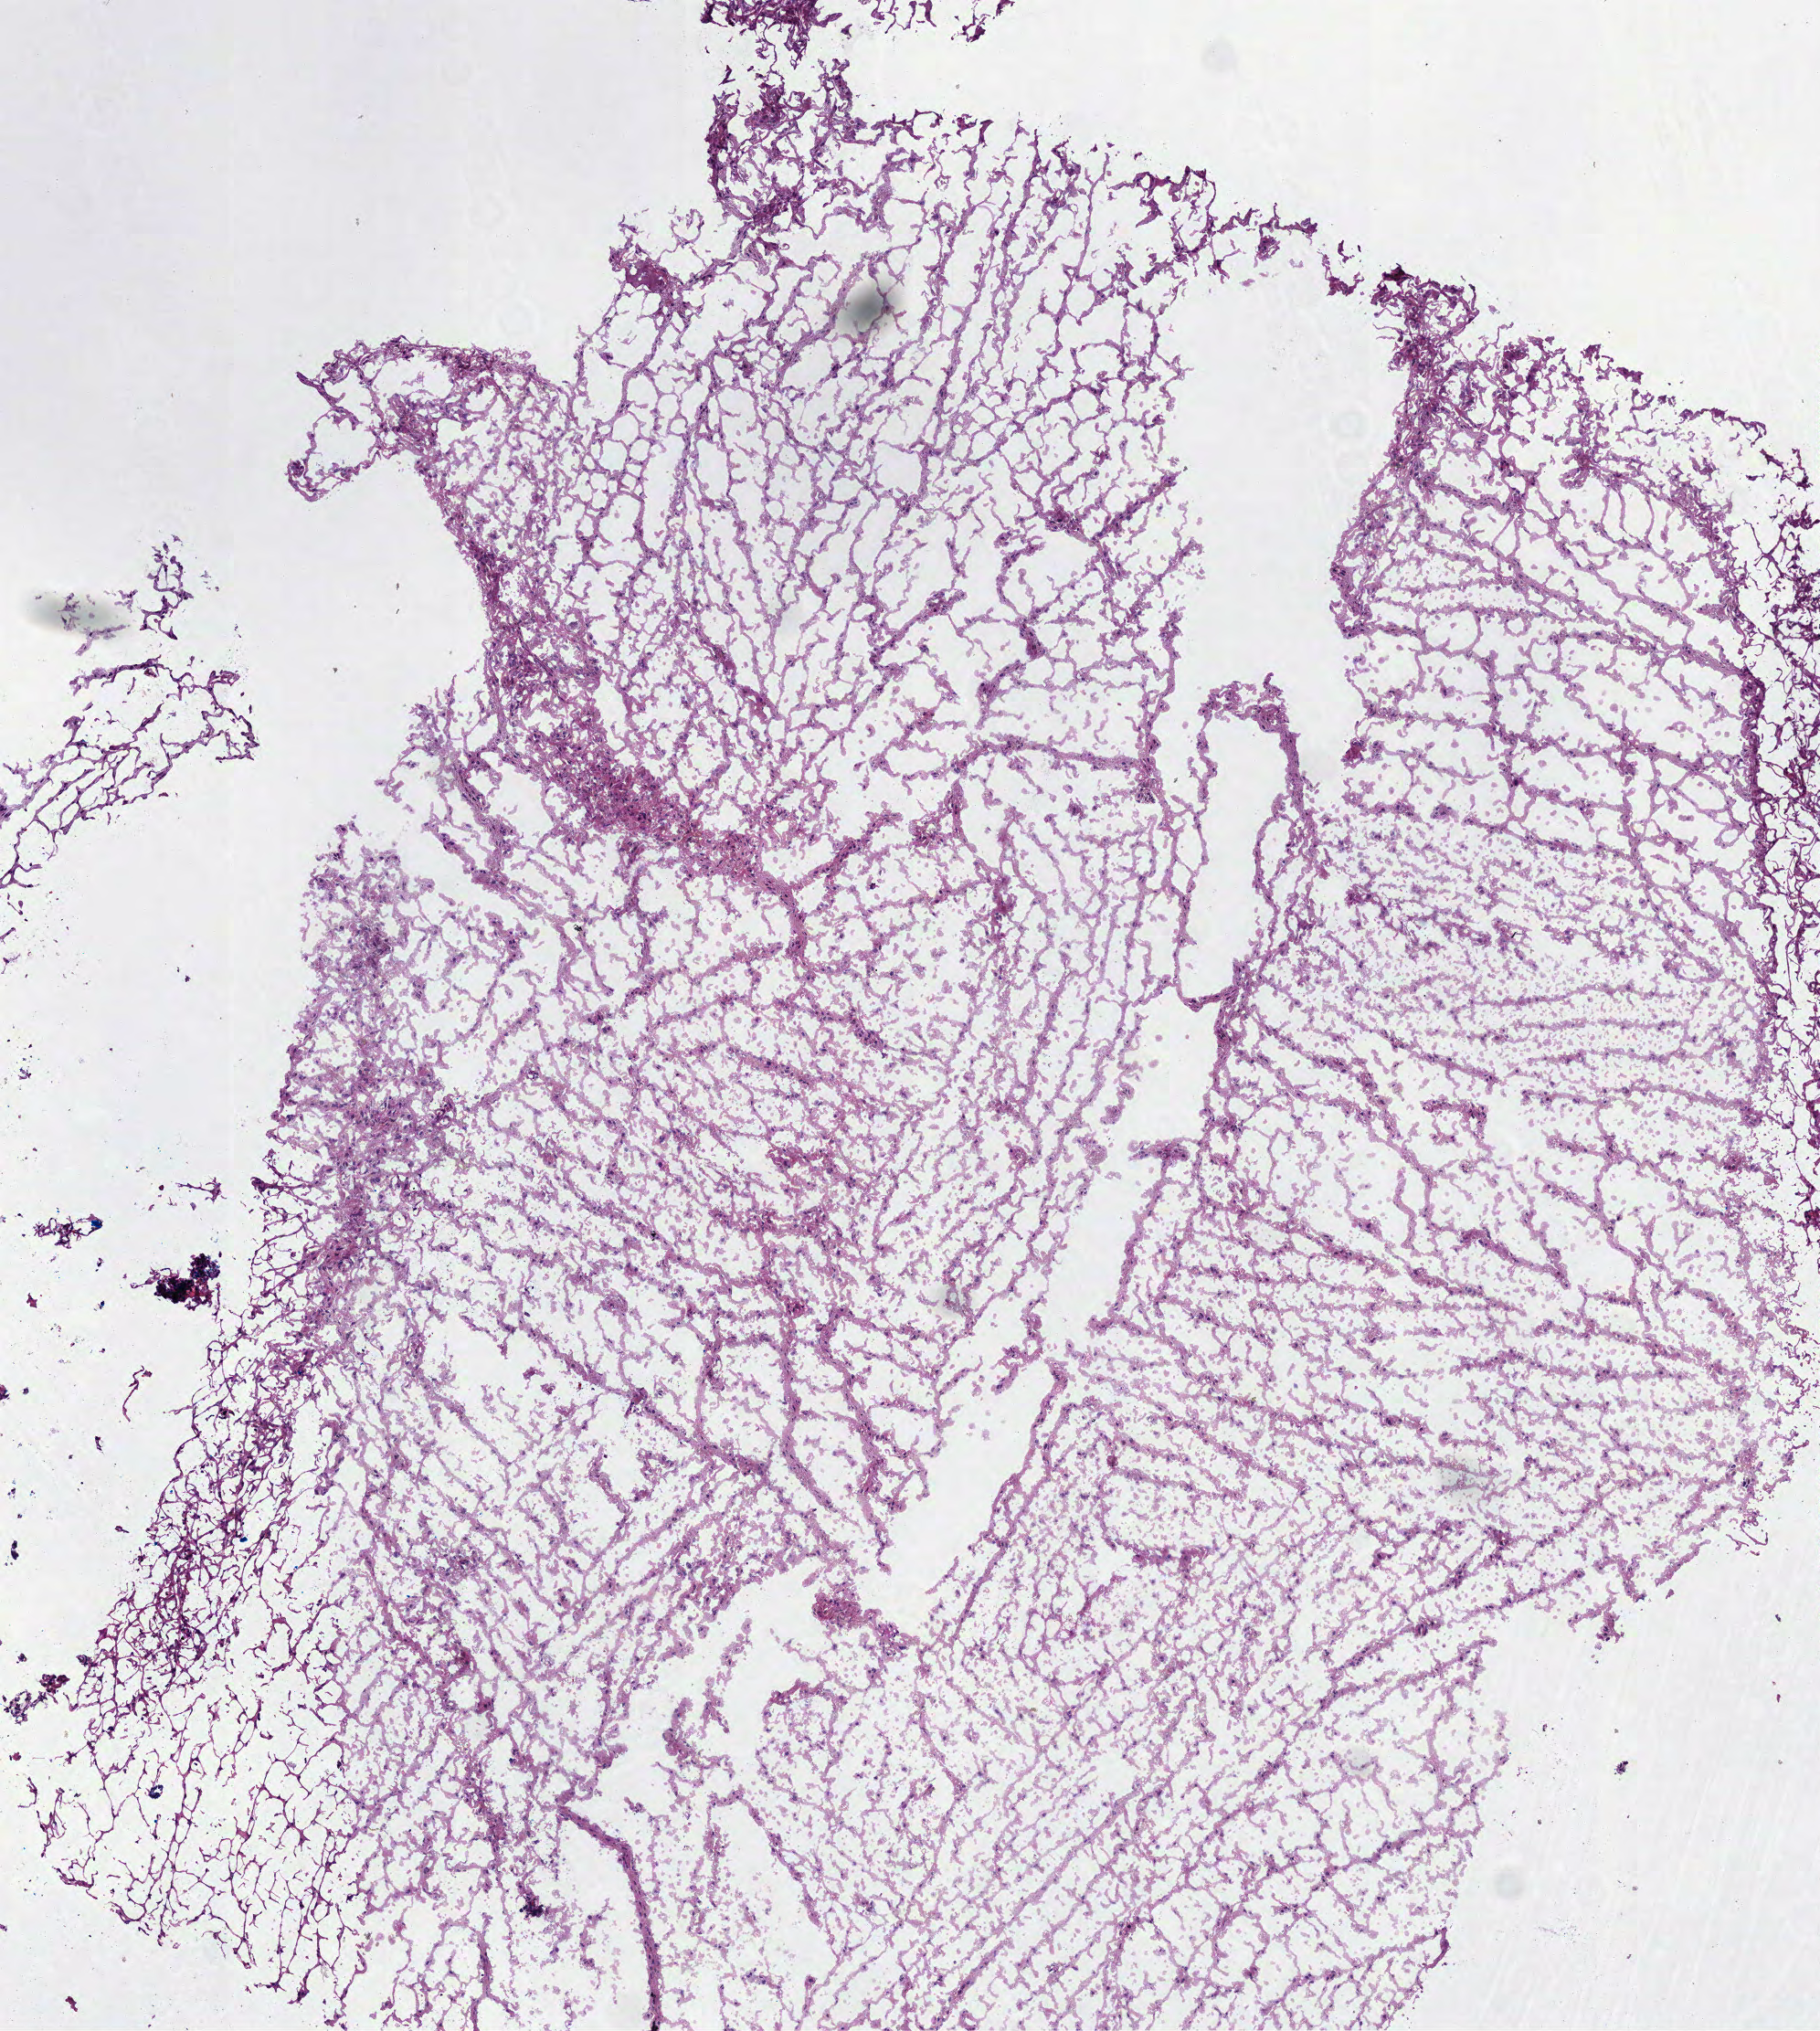
Whole-slide histology image, H&E-stained, shown as a low-resolution overview of the whole scanned area (about 4.0 x 4.5 mm, from a 40x scan), frozen section, sample: primary tumour, brain. Female patient; age at initial diagnosis 31 years. Histologic grade: G2 (moderately differentiated). Composition of this section per pathologist review: tumour cells 100%, tumour nuclei 65%, normal cells 0%, stromal cells 0%, necrosis 0%.
- diagnosis: Astrocytoma, NOS